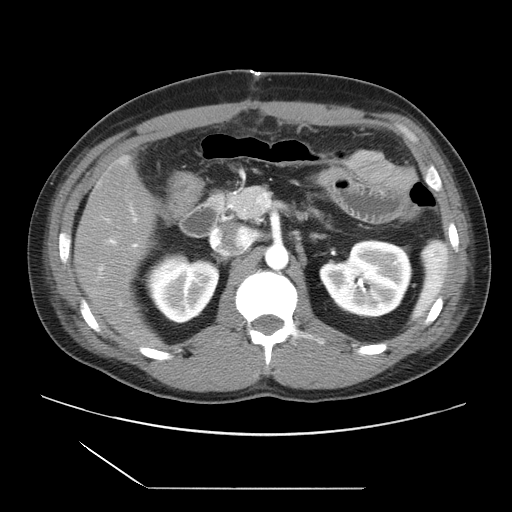
Contrast-enhanced abdominal CT, one axial slice; position 10 of 39 along the scan axis; intravenous contrast given; soft-tissue window (W 400 / L 40 HU); 5 mm slice thickness; 512 × 512 image matrix. Male patient, age 39 years. Case-level facts recorded for this patient, not image findings: diagnosis: colorectal cancer liver metastases, imaged before liver resection; multiple liver metastases: yes; largest metastasis: 1.3 cm; disease in both lobes: no.
Structures marked on this image (expert manual segmentation):
- hepatic veins: box from (x=216, y=229) to (x=245, y=255) px
- liver: (x=76, y=158)–(x=160, y=350)
- portal vein (with intrahepatic branches): (x=98, y=207)–(x=138, y=273)